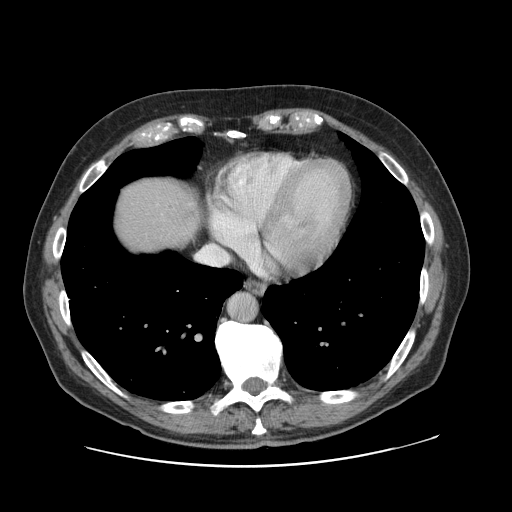
Contrast-enhanced abdominal CT, one axial slice. Slice 115 of 138 in the series (ordered by position). 120 kVp. Intravenous contrast given. Soft-tissue window (W 400 / L 40 HU). 512 × 512 image matrix, field of view 402 × 402 mm. Male patient, age 71 years. From the clinical record (not read from this slice): diagnosis: colorectal cancer liver metastases, imaged before liver resection; multiple liver metastases: no; largest metastasis: 3.3 cm; disease in both lobes: no.
Annotated regions visible in this slice (outlined manually by an expert reader):
- liver: bounding box <112,176,200,256> (left, top, right, bottom; pixels)
- planned liver remnant (the part of the liver to remain after resection): <112,177,199,255>